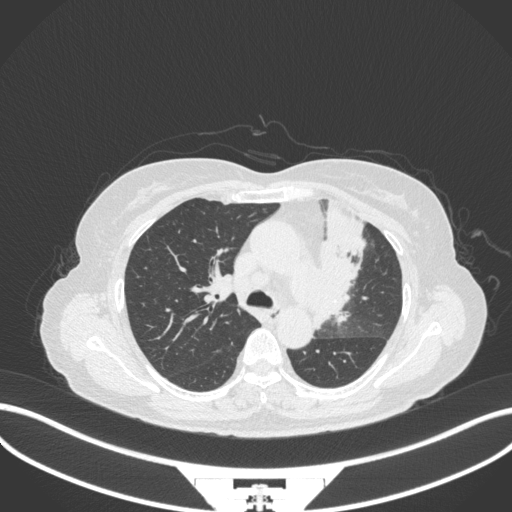
Chest CT, one axial slice. Lung window (W 1500 / L -600 HU). 1 mm slice thickness. 512 × 512 image matrix. Female patient, age 64 years. From the clinical record (not read from this slice): clinical TNM (as recorded): T2a N2 M0.
Outlined on this slice (rectangle marked by the reading radiologist):
- lung tumour (recorded histology: adenocarcinoma): bounding box [x1, y1, x2, y2] px = [310, 196, 370, 334]